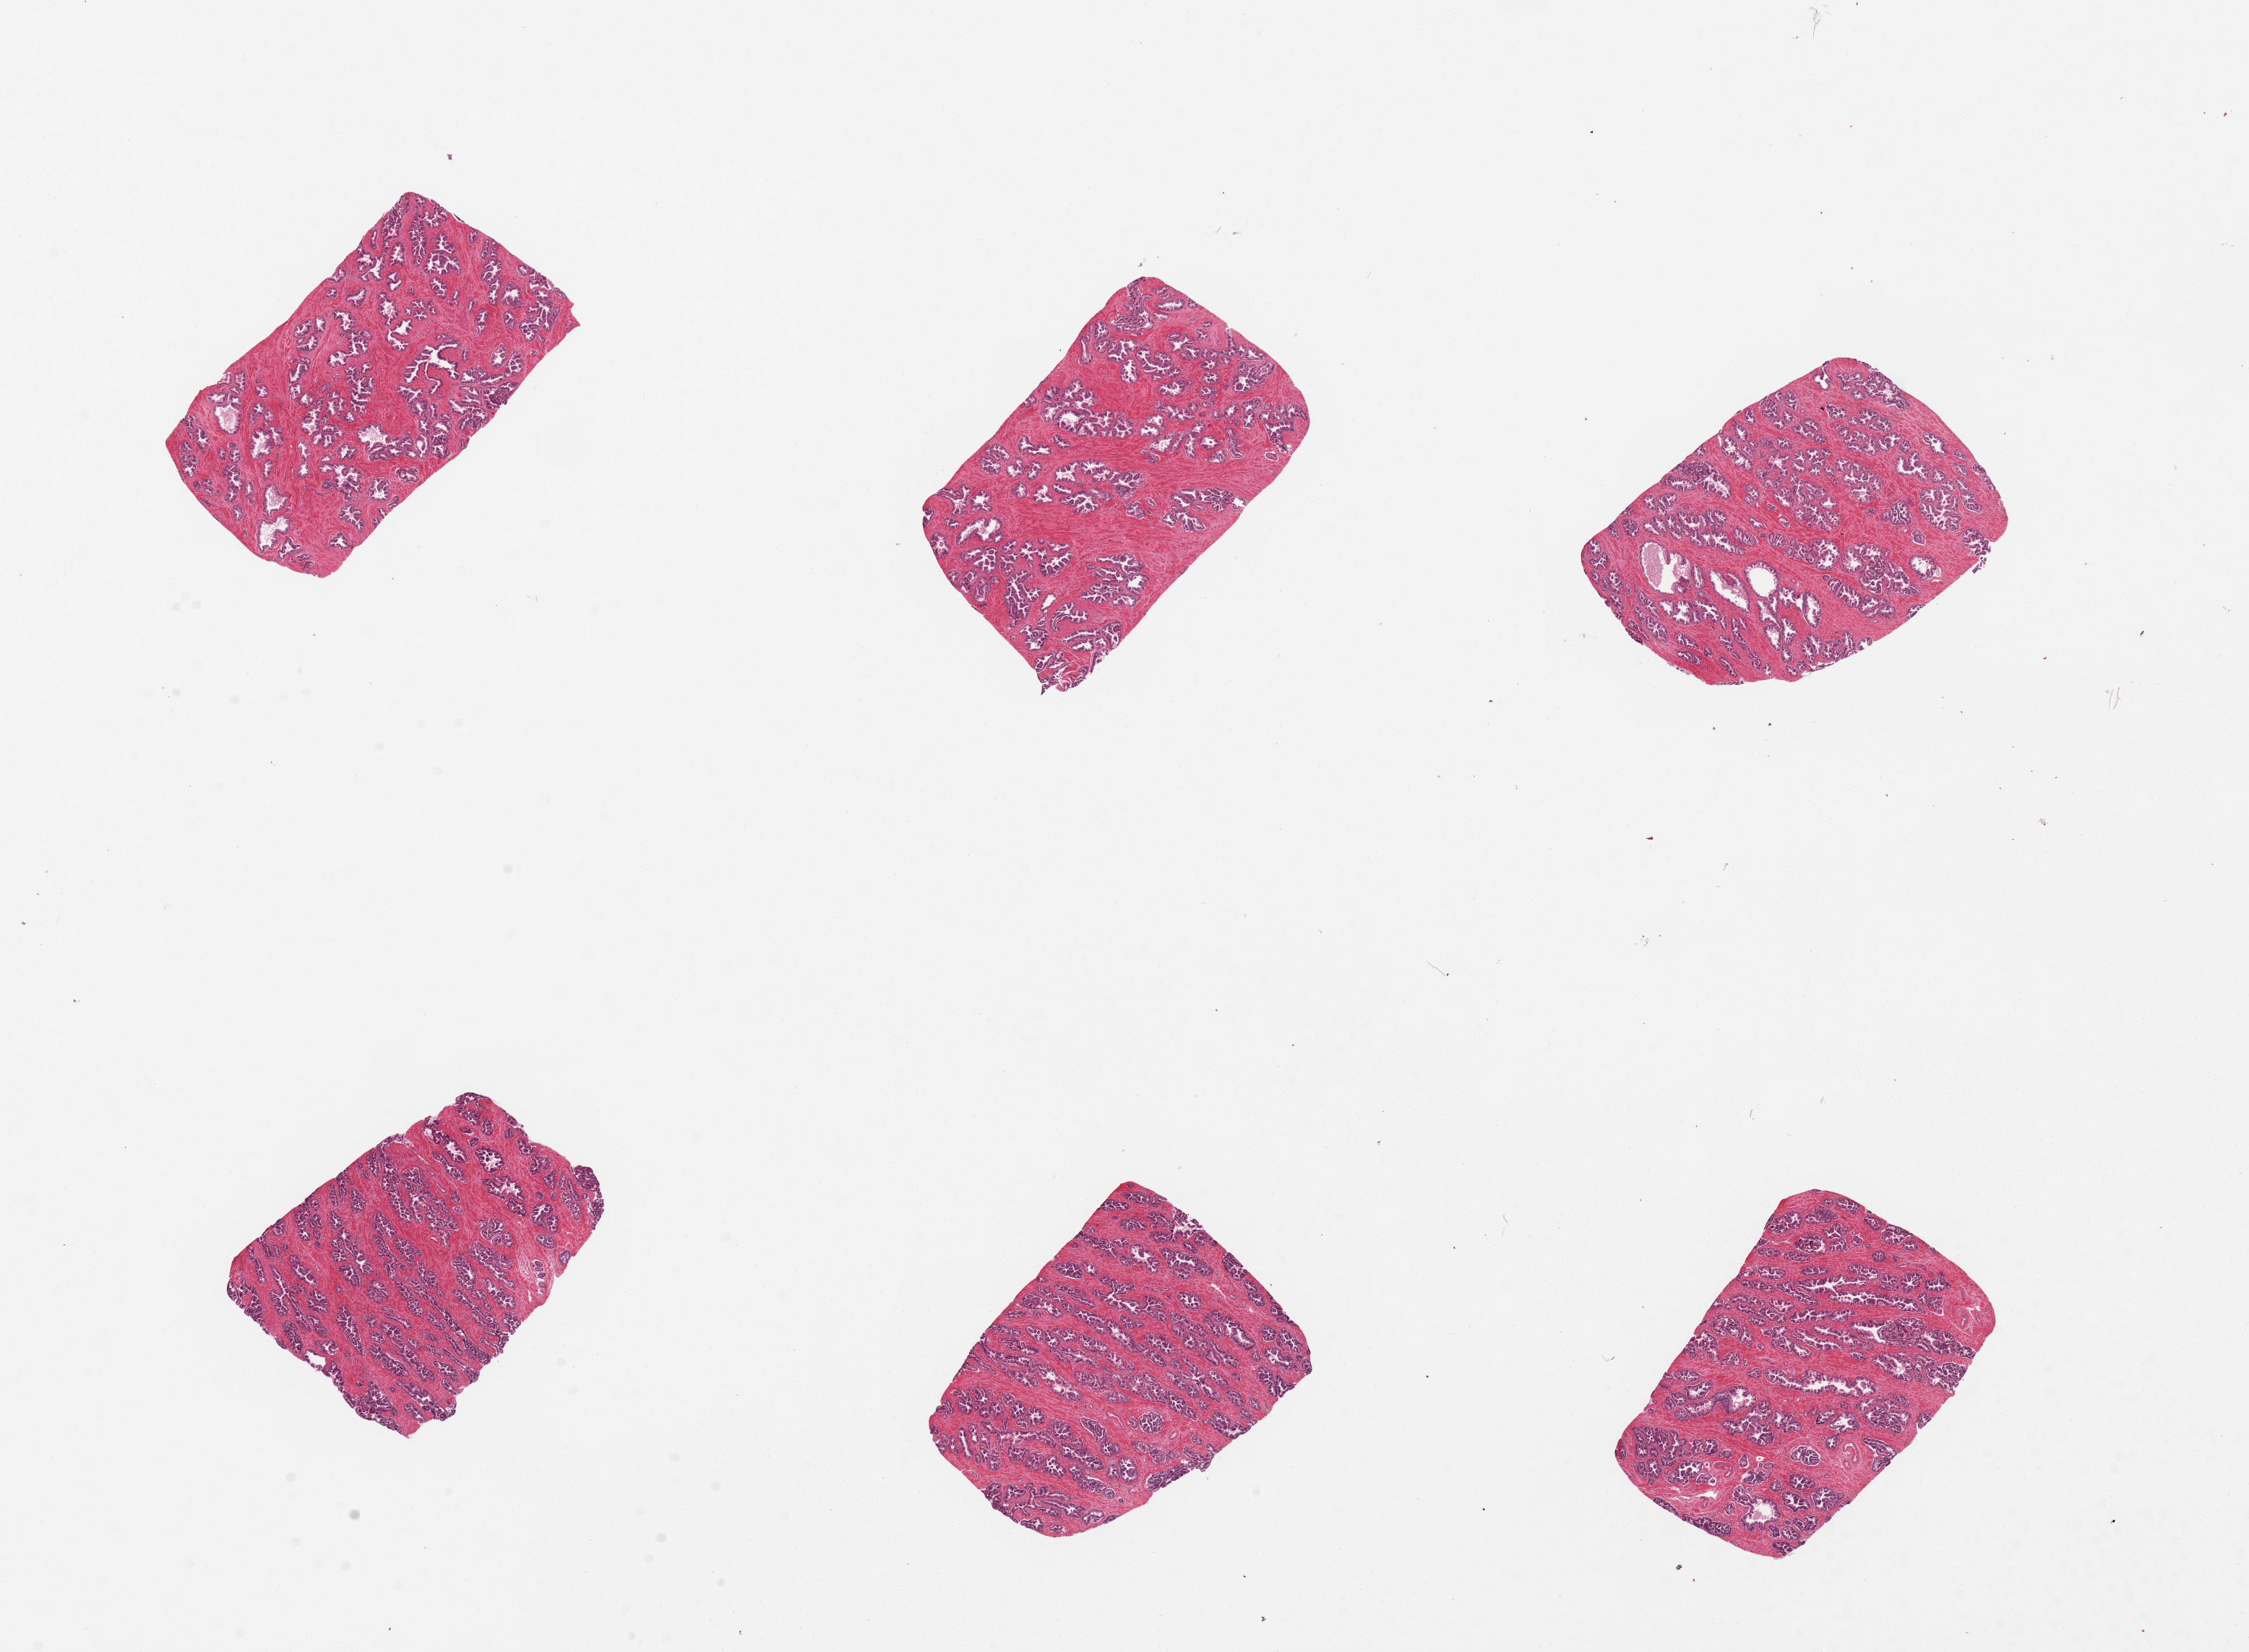
Whole-slide image, H&E stain, brightfield, low-resolution overview of the scanned area, about 24.6 x 18.1 mm; PAXgene-fixed, paraffin-embedded tissue; section of prostate (target tissue); donor tissue sample. Donor sex: male.
Pathologist's review note for this sample: 6 pieces; exceptional glandular preservation.